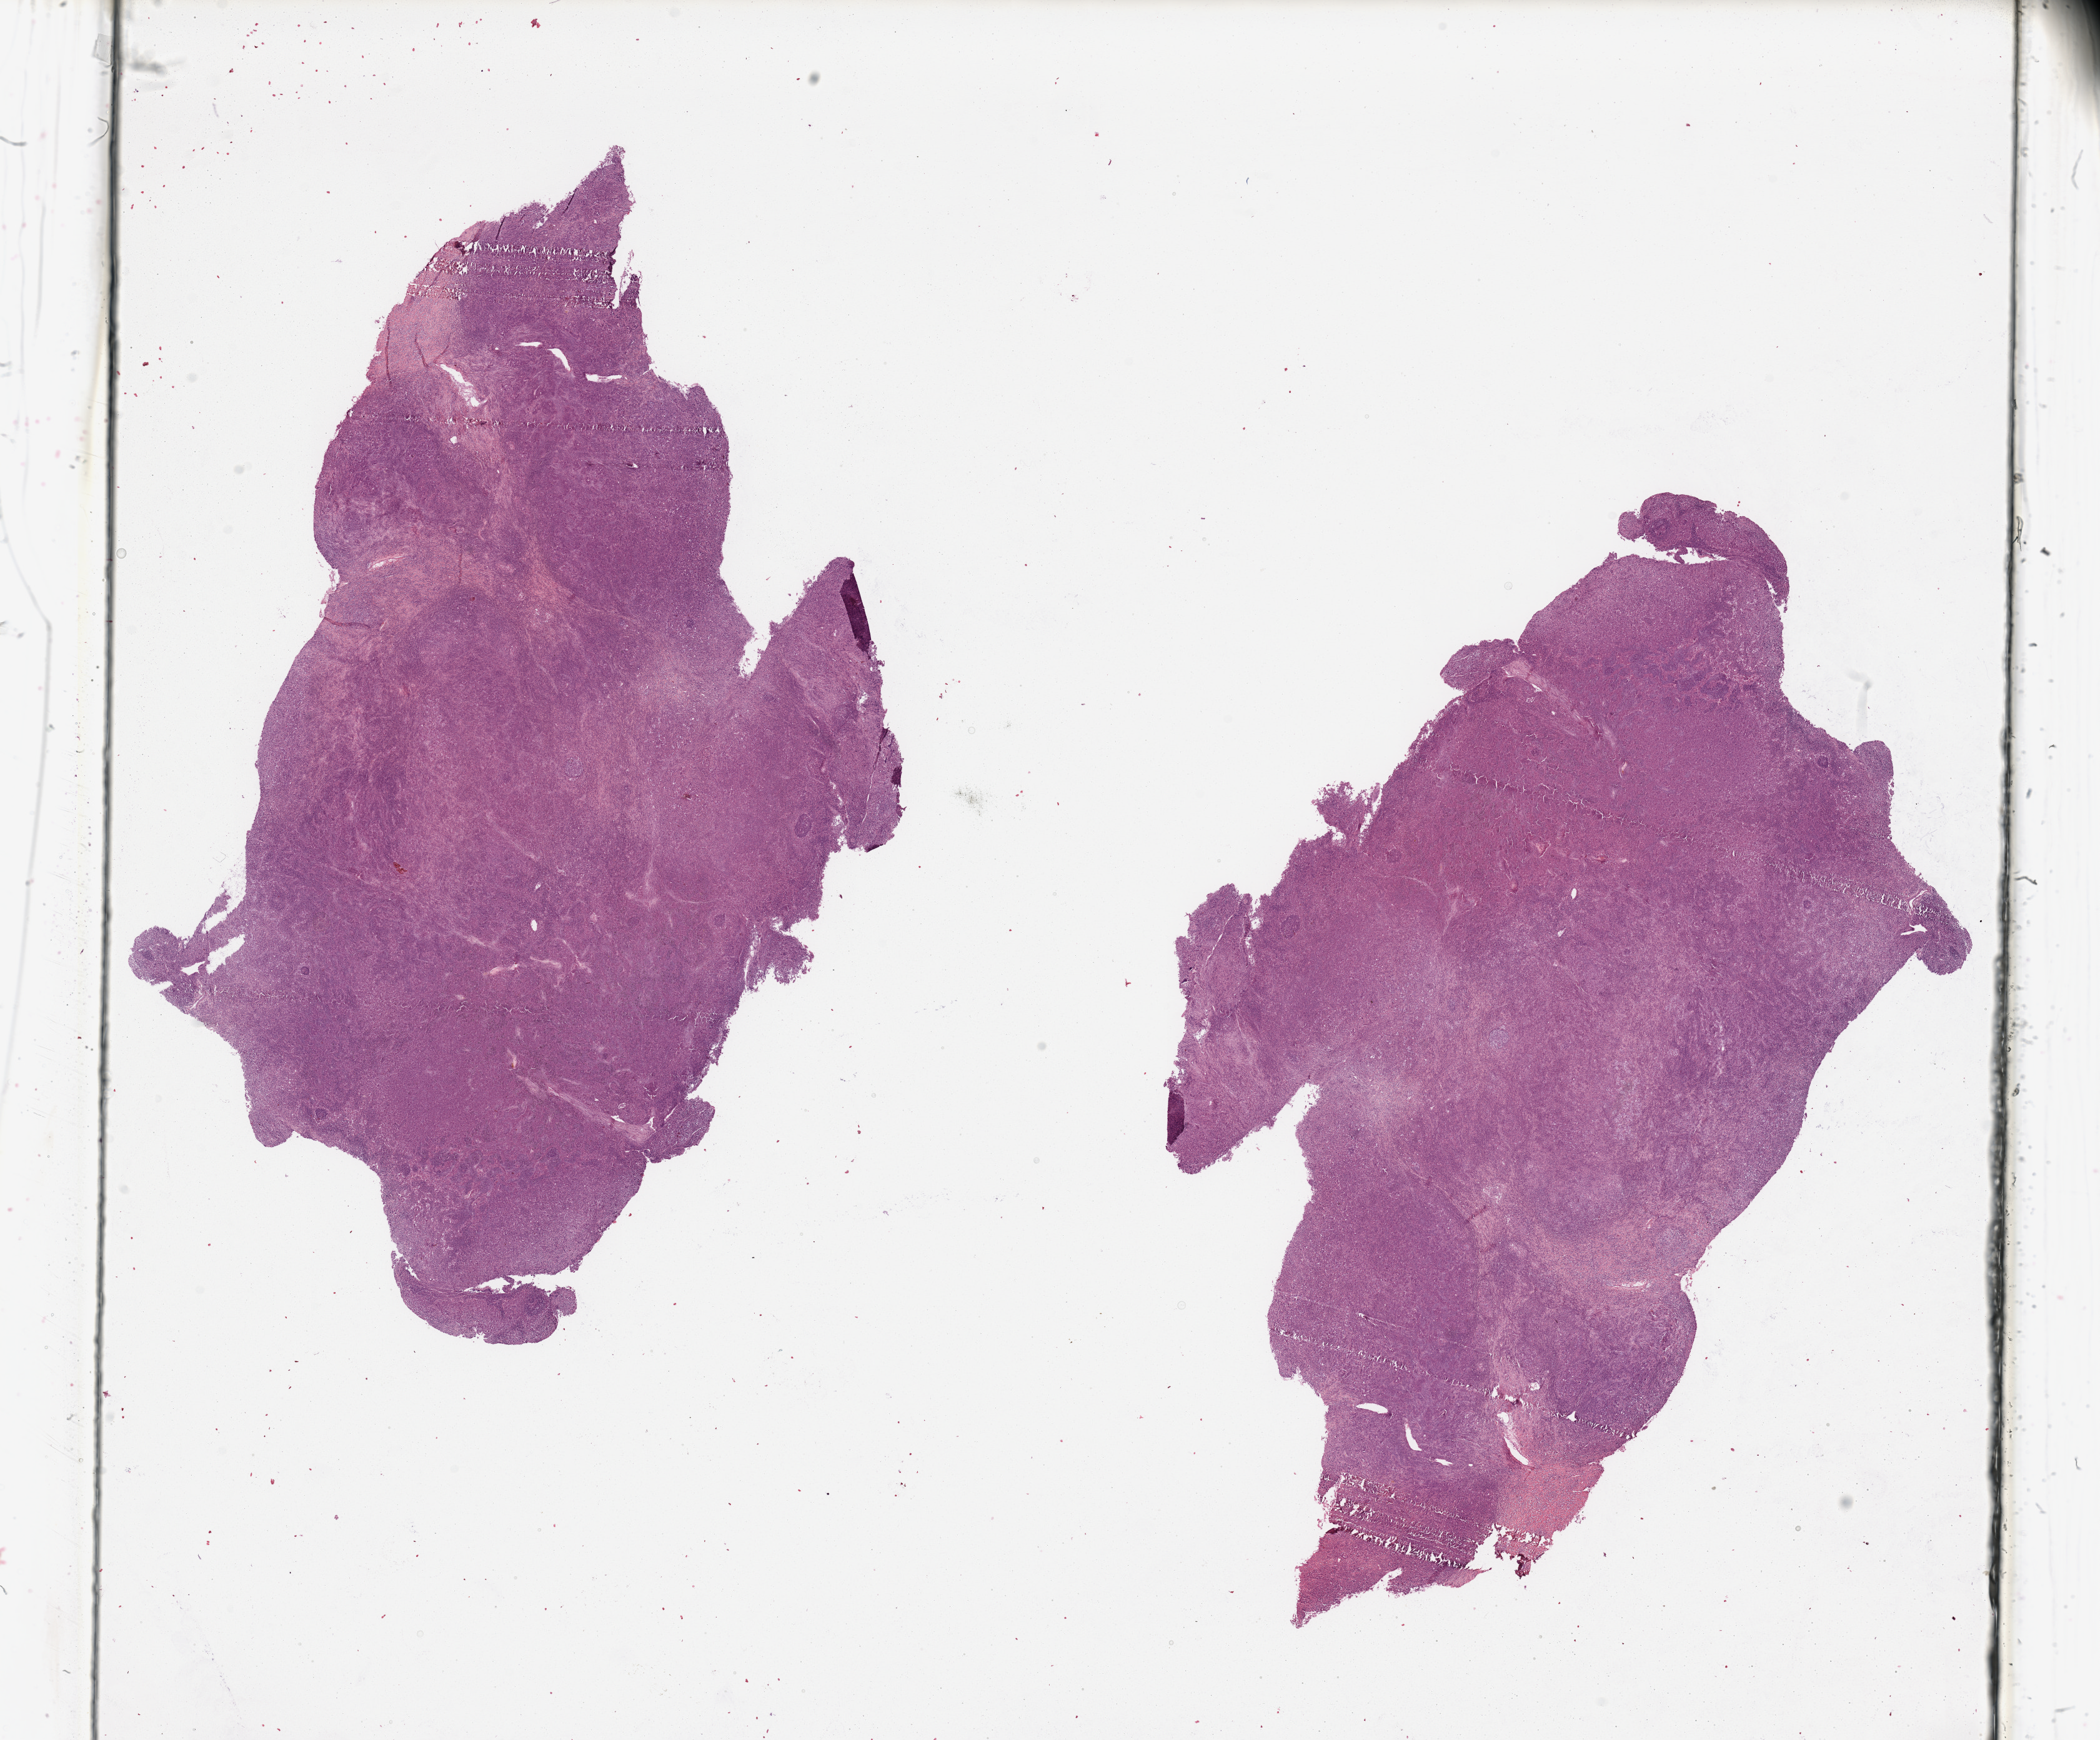
Digitized Hematoxylin and eosin (H&E) stained tissue section (whole slide) — shown as a low-resolution overview of the whole scanned area (about 26.6 x 22.0 mm), tumour tissue sample, sampled site: trunk. 53-year-old female patient. Composition of this section per pathologist review: tumour nuclei 90%, necrosis 0%.
* primary tumour site (as recorded): trunk
* AJCC pathologic stage: IIIB
* diagnosis: Malignant melanoma, NOS